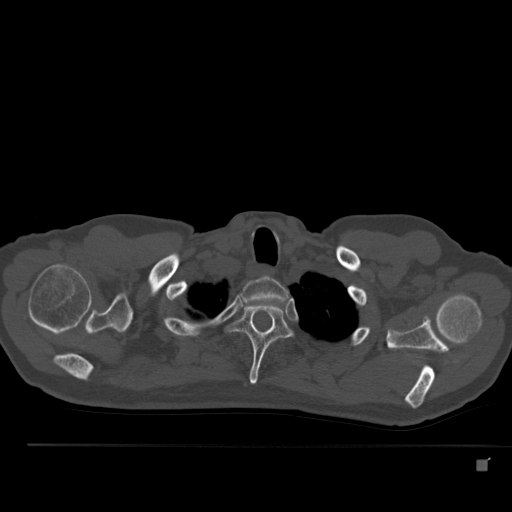
CT including the spine, one axial slice. Position 414 of 517 along the scan axis. Reconstruction kernel Br40s. 120 kVp. Bone window (W 1800 / L 400 HU). 1.5 mm slice thickness. 512 × 512 image matrix, field of view 408 × 408 mm. Male patient, age 70 years. From the clinical record (not read from this slice): primary cancer: renal.
Outlined on this slice (semi-automatically segmented with operator editing):
- T1 vertebra: bounding box [x1, y1, x2, y2] px = [242, 276, 288, 303]
- T2 vertebra: [225, 302, 291, 385]